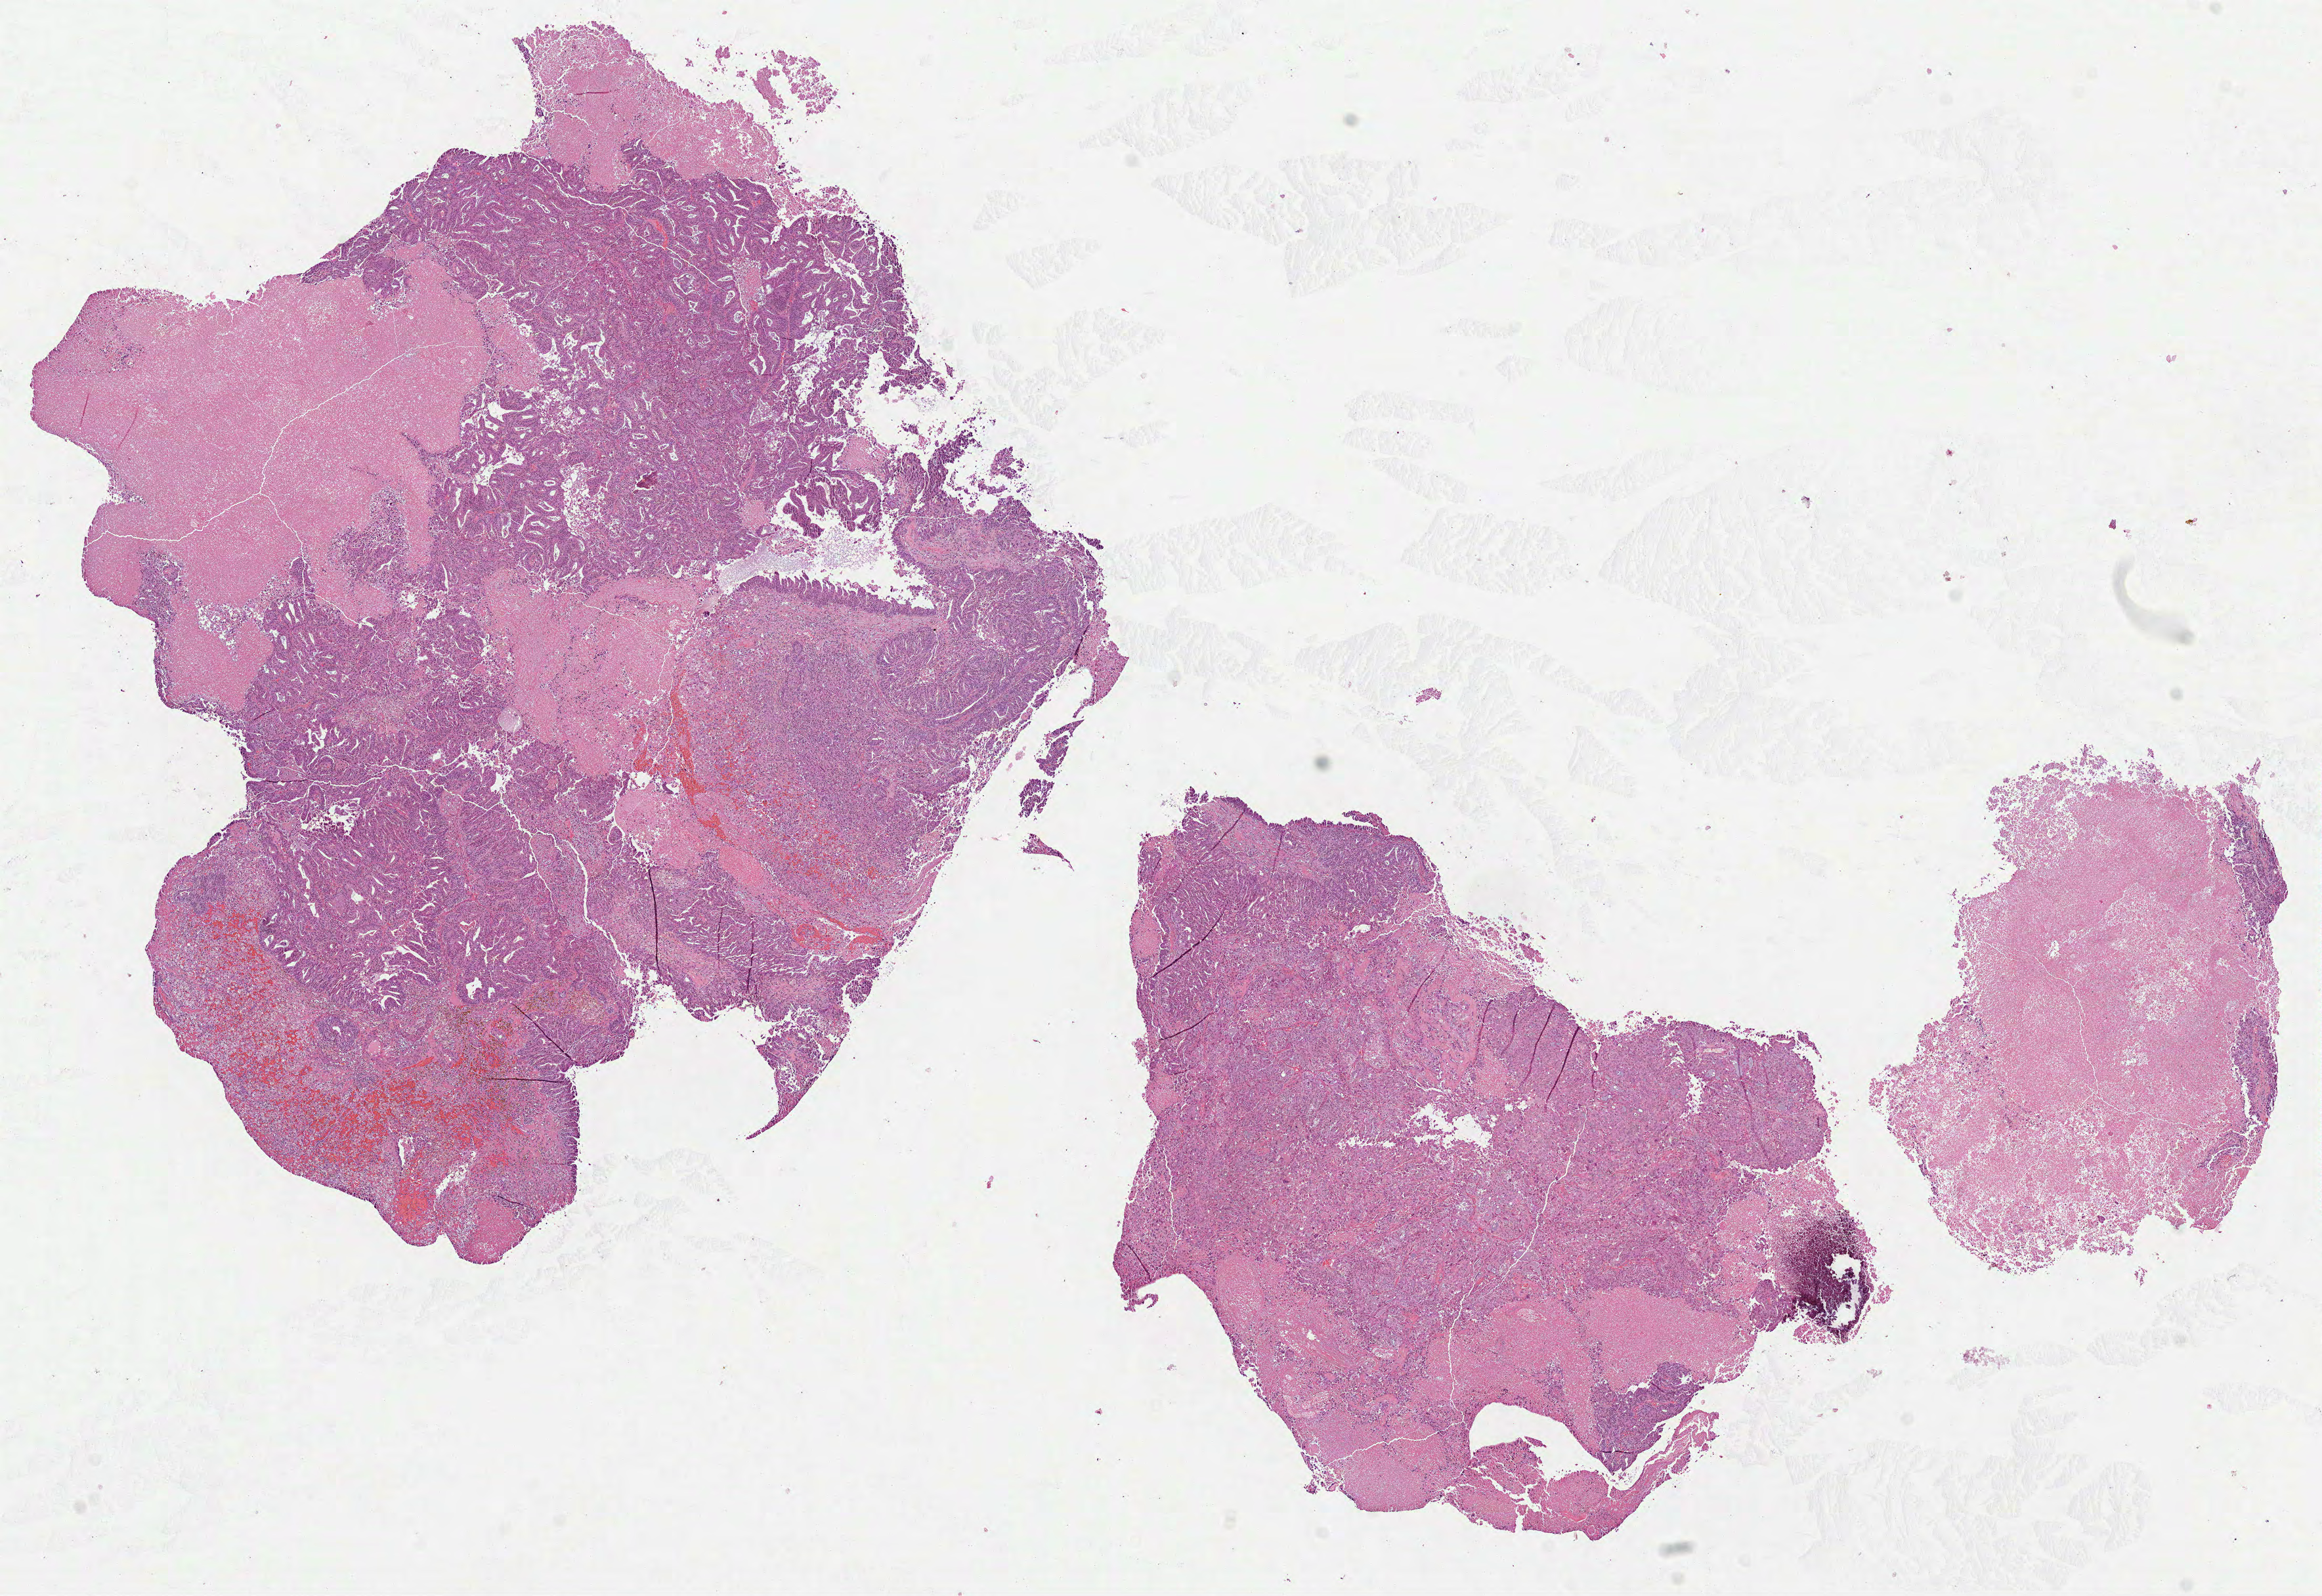
Digitized Hematoxylin and eosin (H&E) stained tissue section (whole slide), whole scanned area (about 14.3 x 9.8 mm) shown as a low-resolution overview; formalin-fixed paraffin-embedded (FFPE) diagnostic section; primary tumour sample from the uterus. Female patient; age at initial diagnosis 65 years. Histologic grade: G3 (poorly differentiated).
• pathologic diagnosis: Endometrioid adenocarcinoma, NOS
• FIGO stage: IA